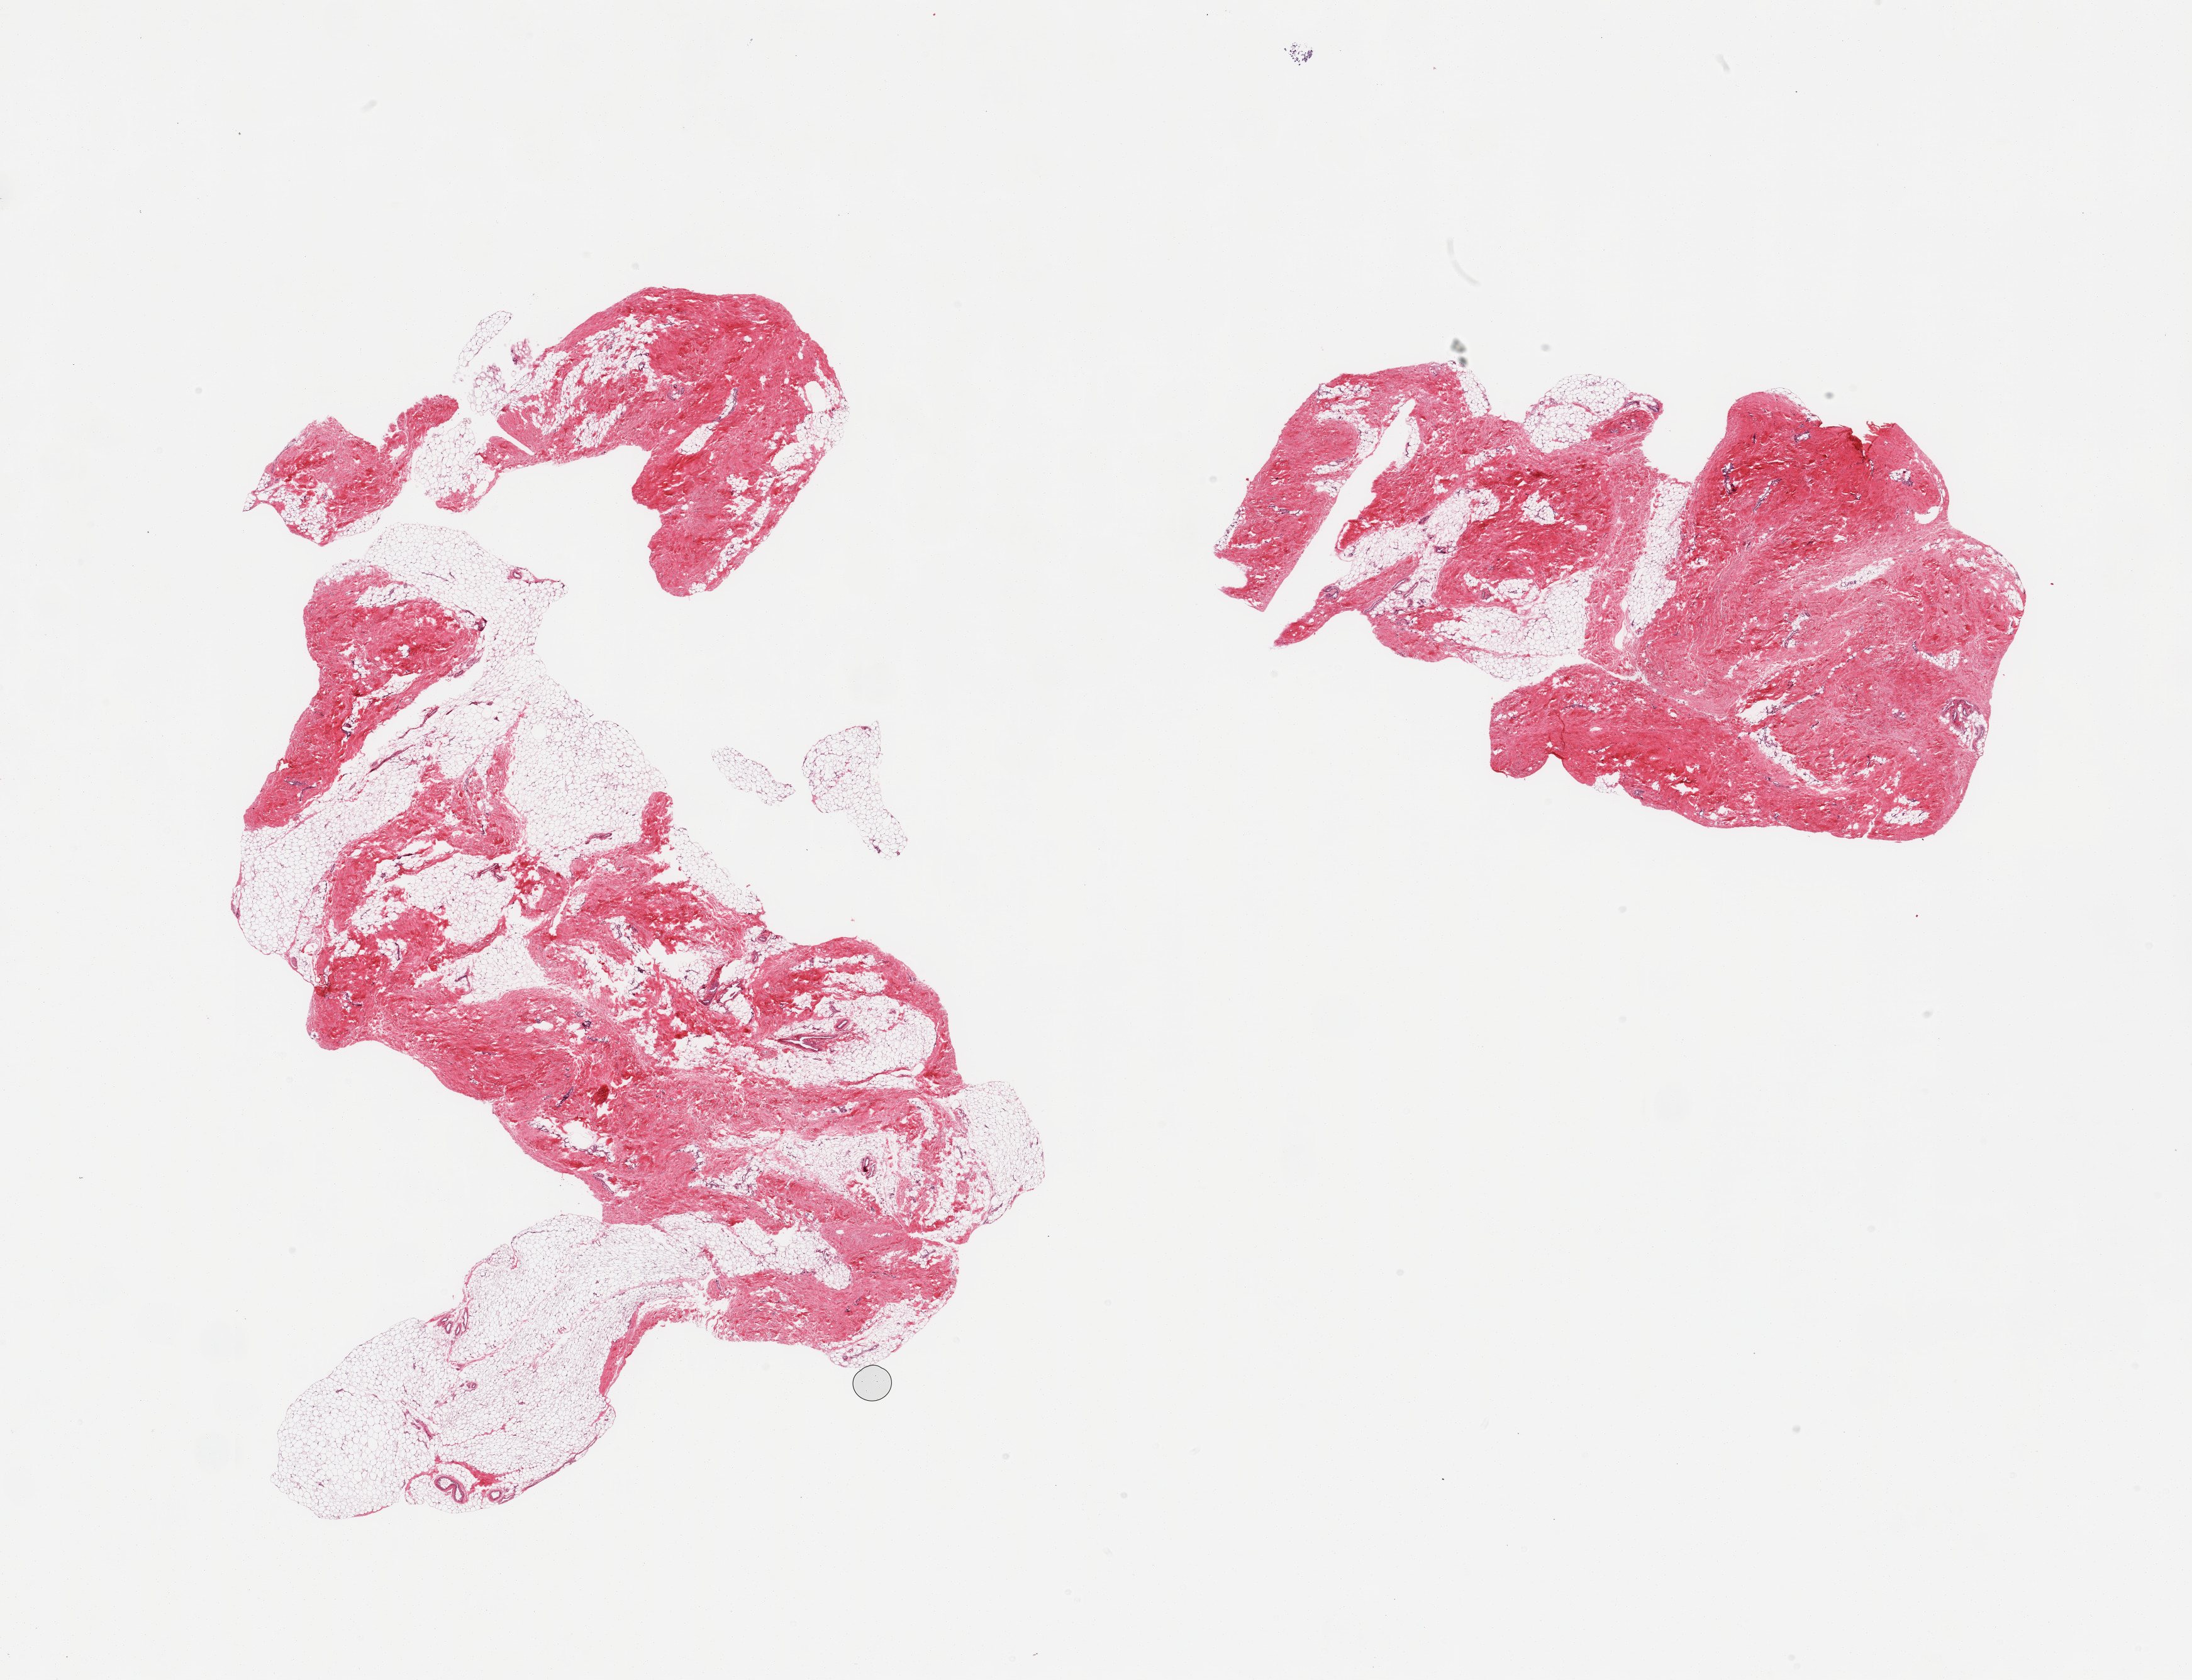
Haematoxylin and eosin whole-slide image — whole scanned area (about 27.6 x 21.1 mm, acquisition: 20x scan) shown as a low-resolution overview; PAXgene-fixed paraffin-embedded (PFPE) section; target tissue: breast; tissue donor sample. Donor: male.
Reviewer comment on this tissue sample: 2 pieces; predominantly dense fibrocollagenous stroma with lesser component of fat (10-30%), no ductal structures in this section.